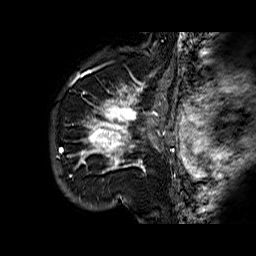
Breast MRI (dynamic contrast-enhanced), one sagittal slice; slice 51 of 60 in the series (ordered by position); dynamic contrast-enhanced series, time point 2 of 6 at this slice position (early post-contrast); 1.5 T; TE 6.3 ms, TR 32.4 ms; 256 × 256 image matrix, field of view 200 × 200 mm. Female patient. Case-level facts recorded for this patient, not image findings: setting: breast cancer imaged before/during neoadjuvant chemotherapy; receptor status: HR-positive, HER2-negative.
Annotated regions visible in this slice (semi-automatically segmented with operator editing):
- analysis volume of interest (the breast-tissue region the enhancement analysis was run in; not a lesion): bounding box (x1, y1, x2, y2) in pixels: (68, 72, 177, 183)
- tumour enhancement mask (voxels above the 100 % enhancement threshold inside the analysis volume of interest): (73, 73, 174, 173)